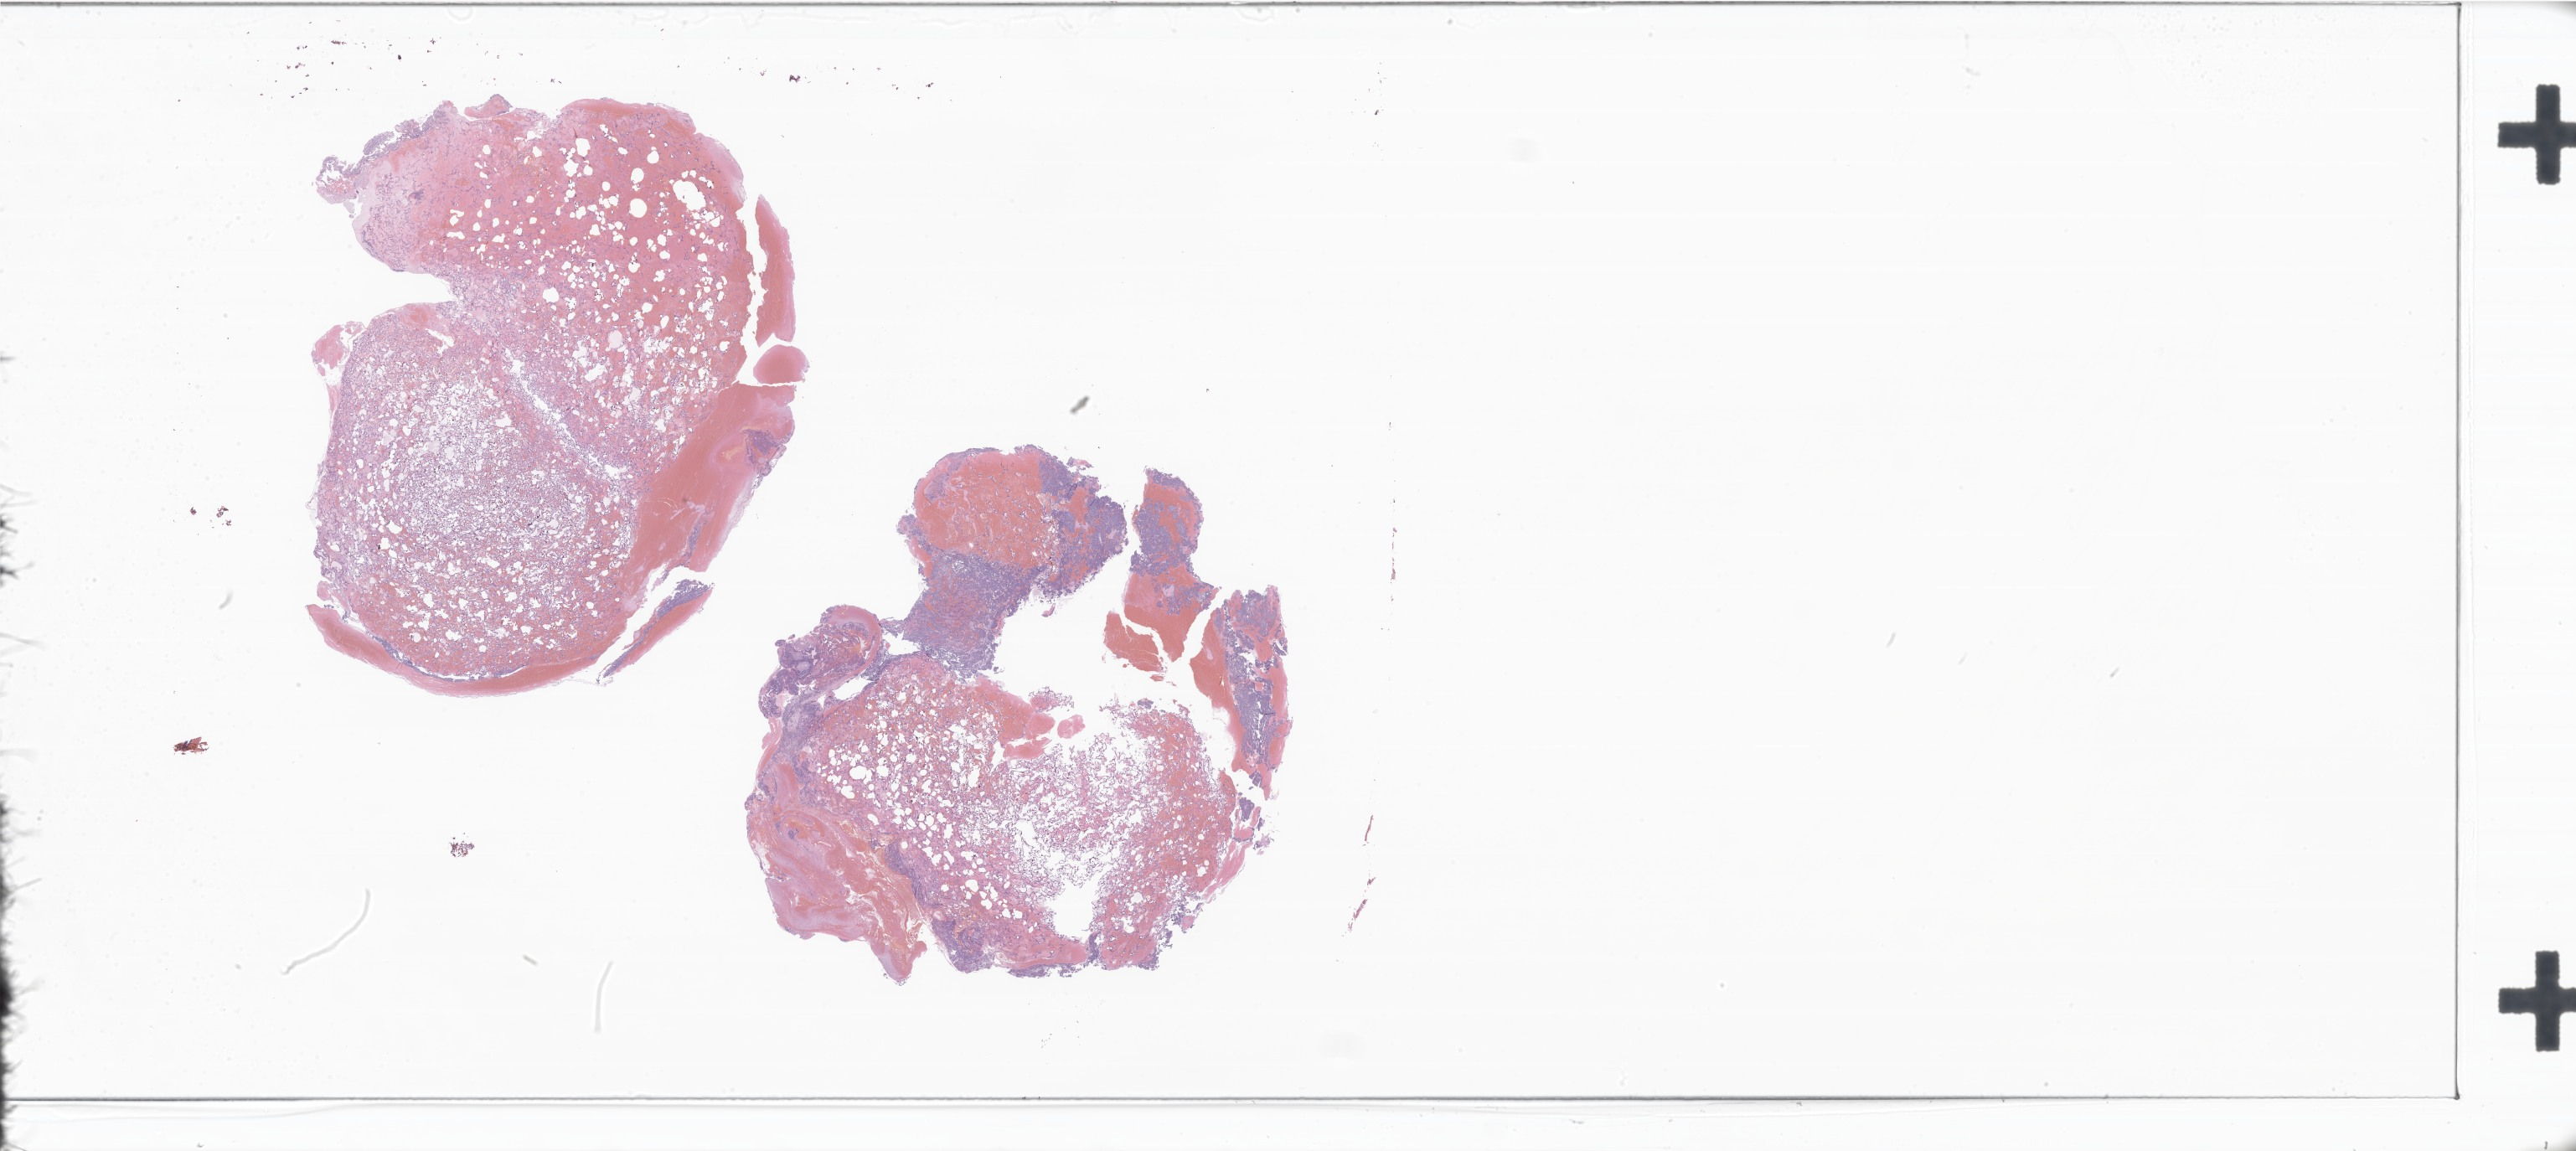
Digitized haematoxylin and eosin-stained section of tumor tissue from the brain — whole scanned area (about 51.9 x 23.2 mm) shown as a low-resolution overview; formalin-fixed paraffin-embedded section. Patient female; age 194 months (16 years 2 months).
Diagnosis: Medulloblastoma, NOS.